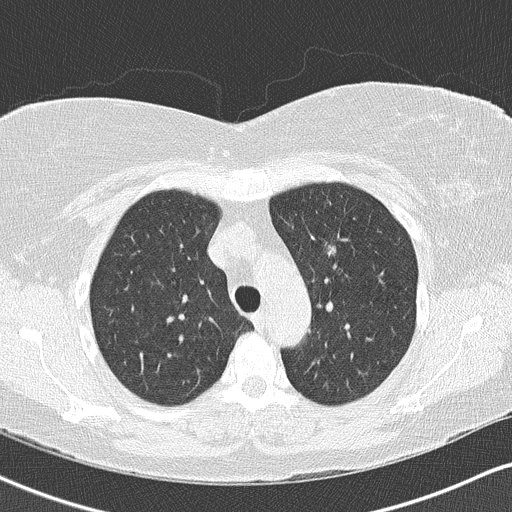
Low-dose screening chest CT, one axial slice; position 110 of 146 along the scan axis; reconstruction kernel B50f; lung window (W 1500 / L -600 HU); 2 mm slice thickness; 512 × 512 image matrix, field of view 328 × 328 mm.
Outlined on this slice (expert manual segmentation):
- lesion 1 (tumor, upper lobe of left lung): bounding box (x1, y1, x2, y2) in pixels: (326, 244, 337, 258)